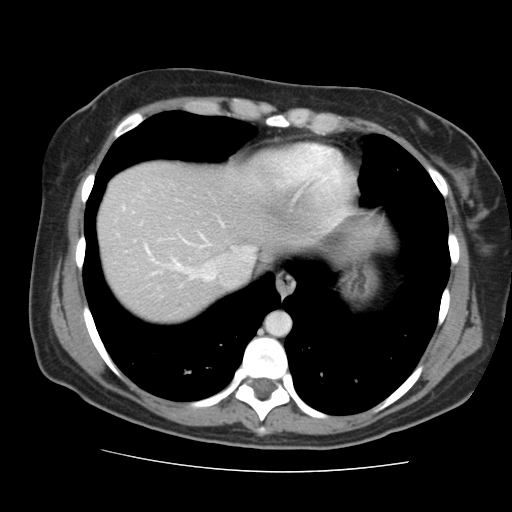
Contrast-enhanced abdominal CT, one axial slice; slice 131 of 144 in the series (ordered by position); intravenous contrast given; soft-tissue window (W 400 / L 40 HU); 2.5 mm slice thickness; 512 × 512 image matrix, field of view 333 × 333 mm. Female patient, age 46 years. From the clinical record (not read from this slice): diagnosis: colorectal cancer liver metastases, imaged before liver resection; multiple liver metastases: no; largest metastasis: 2.8 cm.
Annotated regions visible in this slice (outlined manually by an expert reader):
- hepatic veins: box from (x=174, y=239) to (x=255, y=282) px
- liver: (x=99, y=162)–(x=303, y=321)
- planned liver remnant (the part of the liver to remain after resection): (x=99, y=162)–(x=303, y=321)
- portal vein (with intrahepatic branches): (x=146, y=249)–(x=179, y=266)